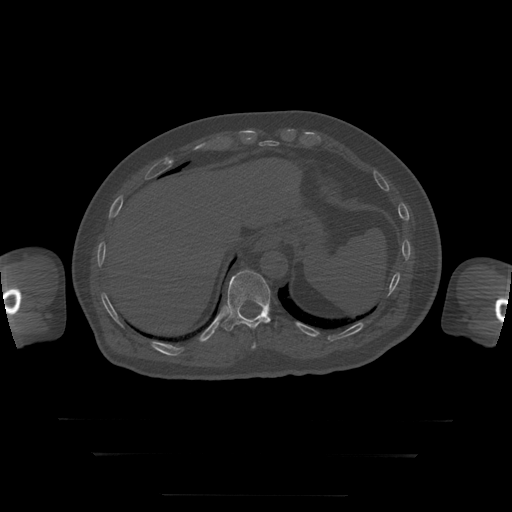
CT including the spine, one axial slice; slice 102 of 397 in the series (ordered by position); bone window (W 1800 / L 400 HU); 512 × 512 image matrix, field of view 510 × 510 mm. Patient age 73 years. From the clinical record (not read from this slice): primary cancer: prostate.
Outlined on this slice (semi-automatically segmented with operator editing):
- T10 vertebra: bounding box <252,343,256,349> (left, top, right, bottom; pixels)
- T11 vertebra: <222,270,271,332>